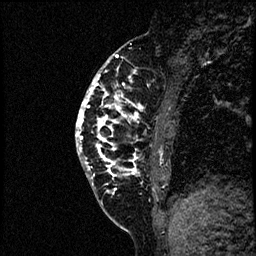
Breast MRI (dynamic contrast-enhanced), one sagittal slice; position 21 of 60 along the scan axis; dynamic contrast-enhanced study with each time point stored as its own series, time point 2 of 4 at this slice position (early post-contrast, ordered by acquisition time); 1.5 T; TE 4.2 ms, TR 17.6 ms; 256 × 256 image matrix, field of view 200 × 200 mm. Female patient, age 40 years. Case-level facts recorded for this patient, not image findings: setting: breast cancer imaged before/during neoadjuvant chemotherapy; receptor status: HER2-positive.
Annotated regions visible in this slice (semi-automatic segmentation, software-assisted and operator-edited):
- analysis volume of interest (the breast-tissue region the enhancement analysis was run in; not a lesion): box from (x=77, y=56) to (x=197, y=205) px
- tumour enhancement mask (voxels above the 100 % enhancement threshold inside the analysis volume of interest): (x=77, y=56)–(x=144, y=179)